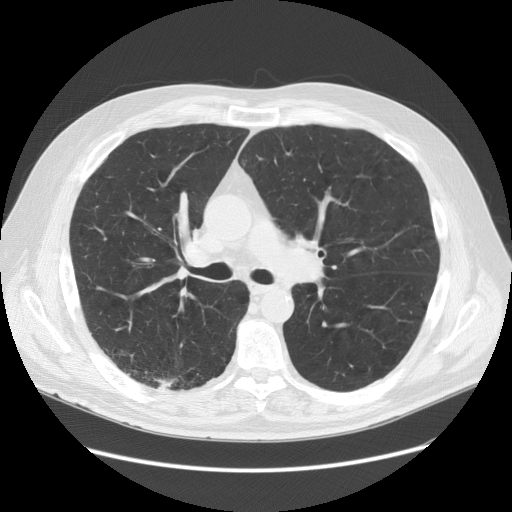
Low-dose screening chest CT, one axial slice. Slice 89 of 149 in the series (ordered by position). Reconstruction kernel STANDARD. 120 kVp. Lung window (W 1500 / L -600 HU). 2.5 mm slice thickness. 512 × 512 image matrix, field of view 400 × 400 mm.
Structures marked on this image (expert manual segmentation):
- lesion 1 (tumor, lower lobe of right lung): bounding box [x1, y1, x2, y2] px = [155, 378, 173, 390]